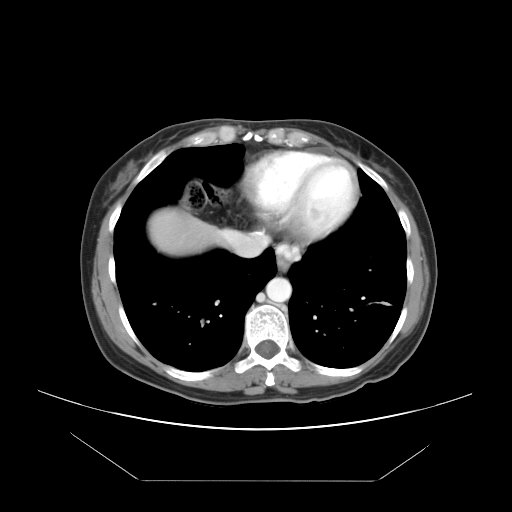
Contrast-enhanced abdominal CT, one axial slice. Slice 42 of 45 in the series (ordered by position). 120 kVp. Intravenous contrast given. Soft-tissue window (W 400 / L 40 HU). 5 mm slice thickness. 512 × 512 image matrix, field of view 405 × 405 mm. Female patient, age 52 years. Case-level facts recorded for this patient, not image findings: diagnosis: colorectal cancer liver metastases, imaged before liver resection; multiple liver metastases: yes; largest metastasis: 2.5 cm; chemotherapy before resection: yes.
Structures marked on this image (outlined manually by an expert reader):
- hepatic veins: bounding box (x1, y1, x2, y2) in pixels: (223, 232, 256, 256)
- liver: (153, 213, 216, 254)
- planned liver remnant (the part of the liver to remain after resection): (153, 213, 217, 253)